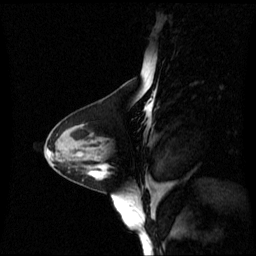
Breast MRI (dynamic contrast-enhanced), one sagittal slice; position 26 of 60 along the scan axis; dynamic contrast-enhanced series, image 2 of 3 at this slice position (ordered by acquisition); 1.5 T; TE 4.2 ms, TR 8.4 ms; 256 × 256 image matrix, field of view 250 × 250 mm. Female patient, age 44 years. Case-level facts recorded for this patient, not image findings: setting: breast cancer imaged before/during neoadjuvant chemotherapy; receptor status: triple-negative.
Outlined on this slice (semi-automatically segmented with operator editing):
- analysis volume of interest (the breast-tissue region the enhancement analysis was run in; not a lesion): bounding box <79,148,132,190> (left, top, right, bottom; pixels)
- tumour enhancement mask (voxels above the 70 % enhancement threshold inside the analysis volume of interest): <92,167,108,177>